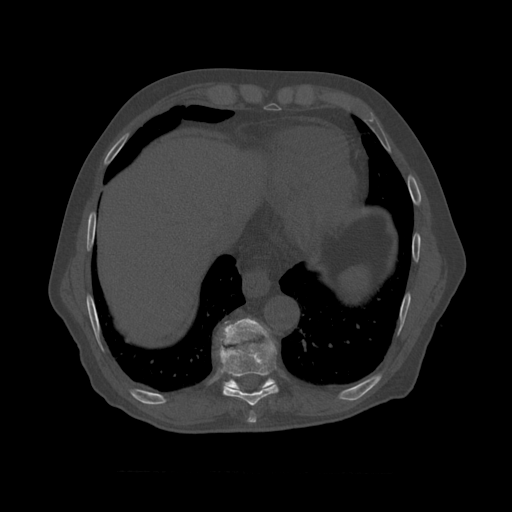
CT including the spine, one axial slice. Position 440 of 450 along the scan axis. 120 kVp. Bone window (W 1800 / L 400 HU). 512 × 512 image matrix, field of view 405 × 405 mm. Patient age 75 years. Case-level facts recorded for this patient, not image findings: primary cancer: prostate.
Annotated regions visible in this slice (semi-automatically segmented with operator editing):
- T8 vertebra: bounding box <218,323,279,407> (left, top, right, bottom; pixels)
- T9 vertebra: <222,318,276,390>